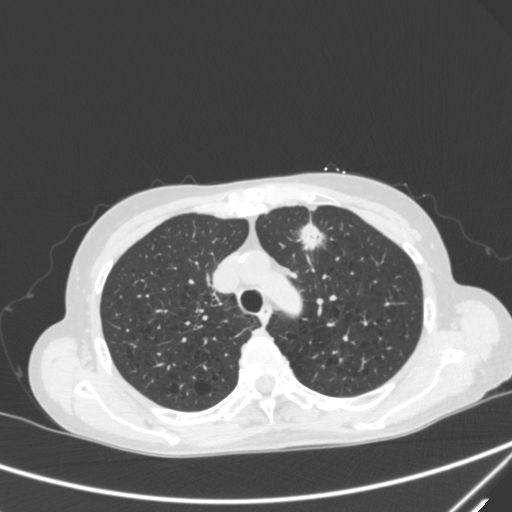
Chest CT, one axial slice. Slice 228 of 300 in the series (ordered by position). Lung window (W 1500 / L -600 HU). 512 × 512 image matrix, field of view 350 × 350 mm. Patient: female, 71 years. From the clinical record (not read from this slice): clinical TNM (as recorded): T1c N0 M0; histopathological grade: G2-3.
Structures marked on this image (bounding box drawn by a radiologist):
- lung tumour (recorded histology: adenocarcinoma): bounding box [x1, y1, x2, y2] px = [296, 218, 331, 259]